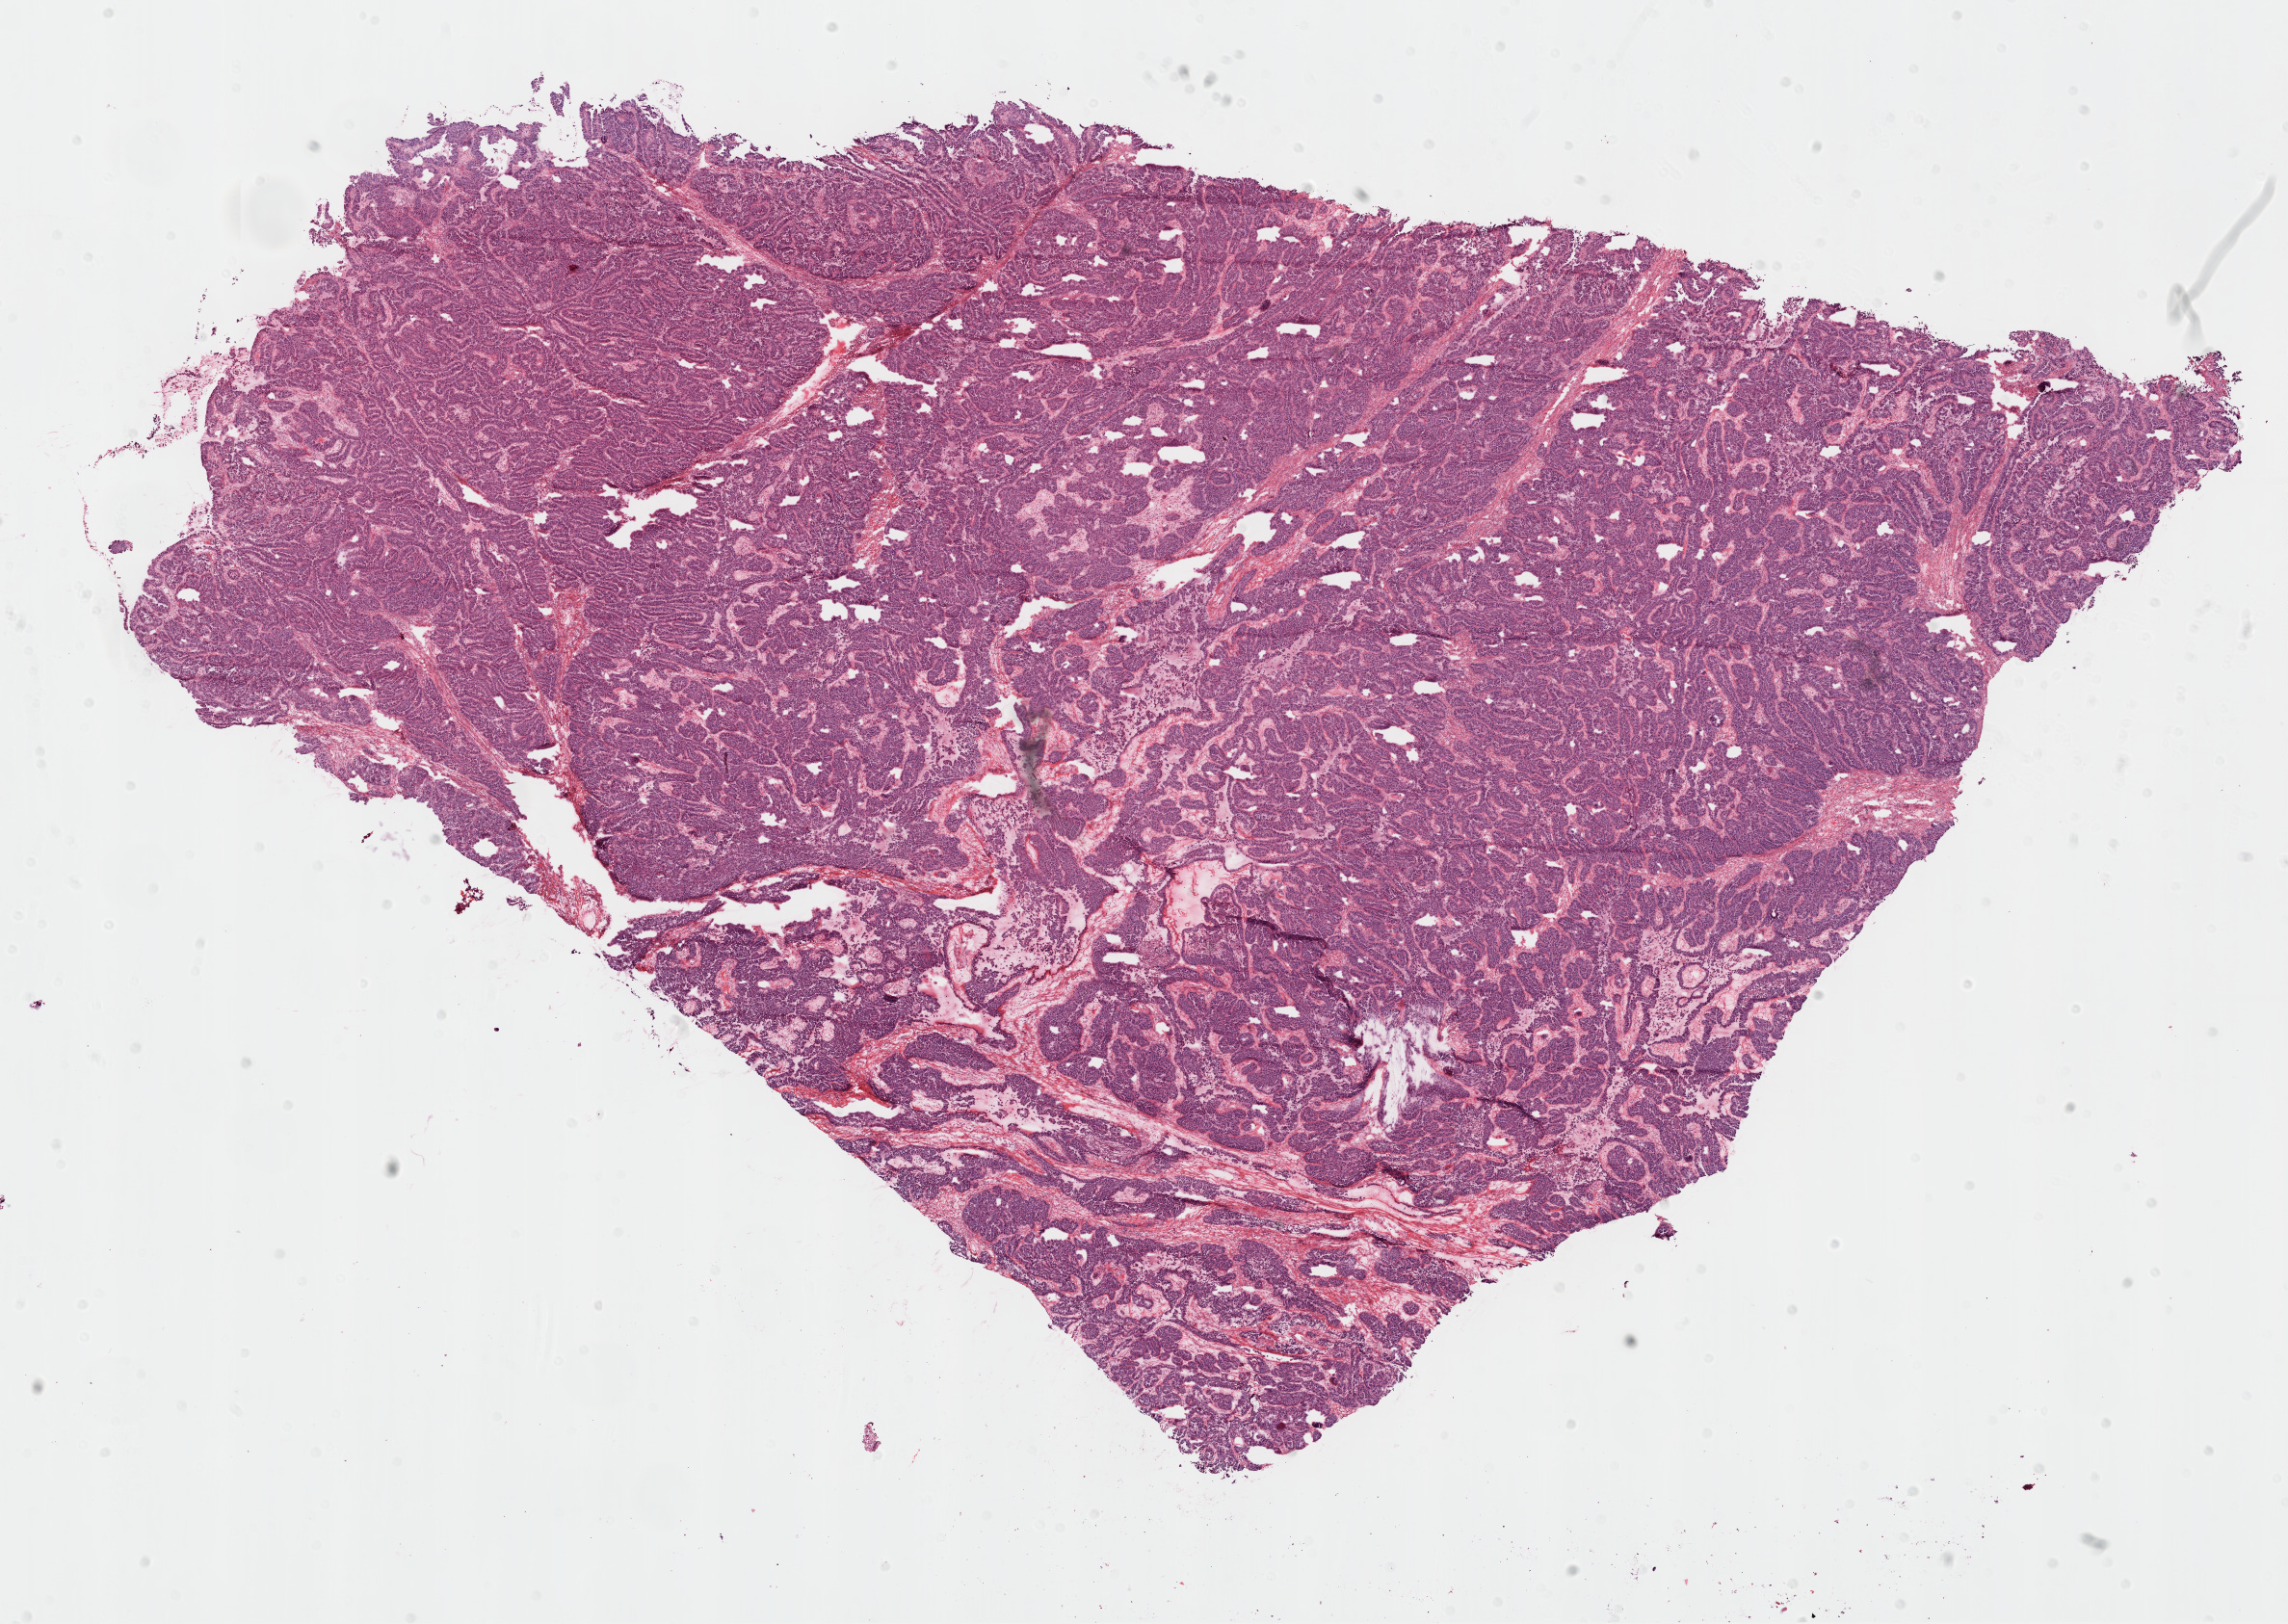
Digitized Hematoxylin and eosin (H&E) stained tissue section (whole slide) — whole scanned area (about 19.1 x 13.5 mm) shown as a low-resolution overview, frozen section from the top of the tissue portion, ovary, primary tumour sample. Female patient; age at initial diagnosis 81 years. Histologic grade: G3 (poorly differentiated). Pathologist review of this section (percent, as recorded): tumour cells 94%, tumour nuclei 95%, normal cells 0%, stromal cells 5%, necrosis 1%.
* FIGO stage: IIIC
* histologic diagnosis: Serous cystadenocarcinoma, NOS